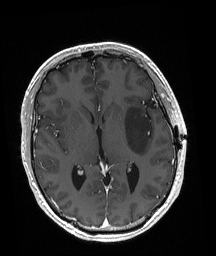
Brain MRI from a brain-tumour surgery series, one axial slice. Position 100 of 192 along the scan axis. T1-weighted post-contrast. 1 mm slice thickness. 216 × 256 image matrix, field of view 211 × 250 mm. From the clinical record (not read from this slice): histopathology: Astrocytoma; WHO grade: 3; IDH mutation: yes.
Structures marked on this image (manually delineated by an expert):
- tumour: box from (x=124, y=107) to (x=152, y=155) px